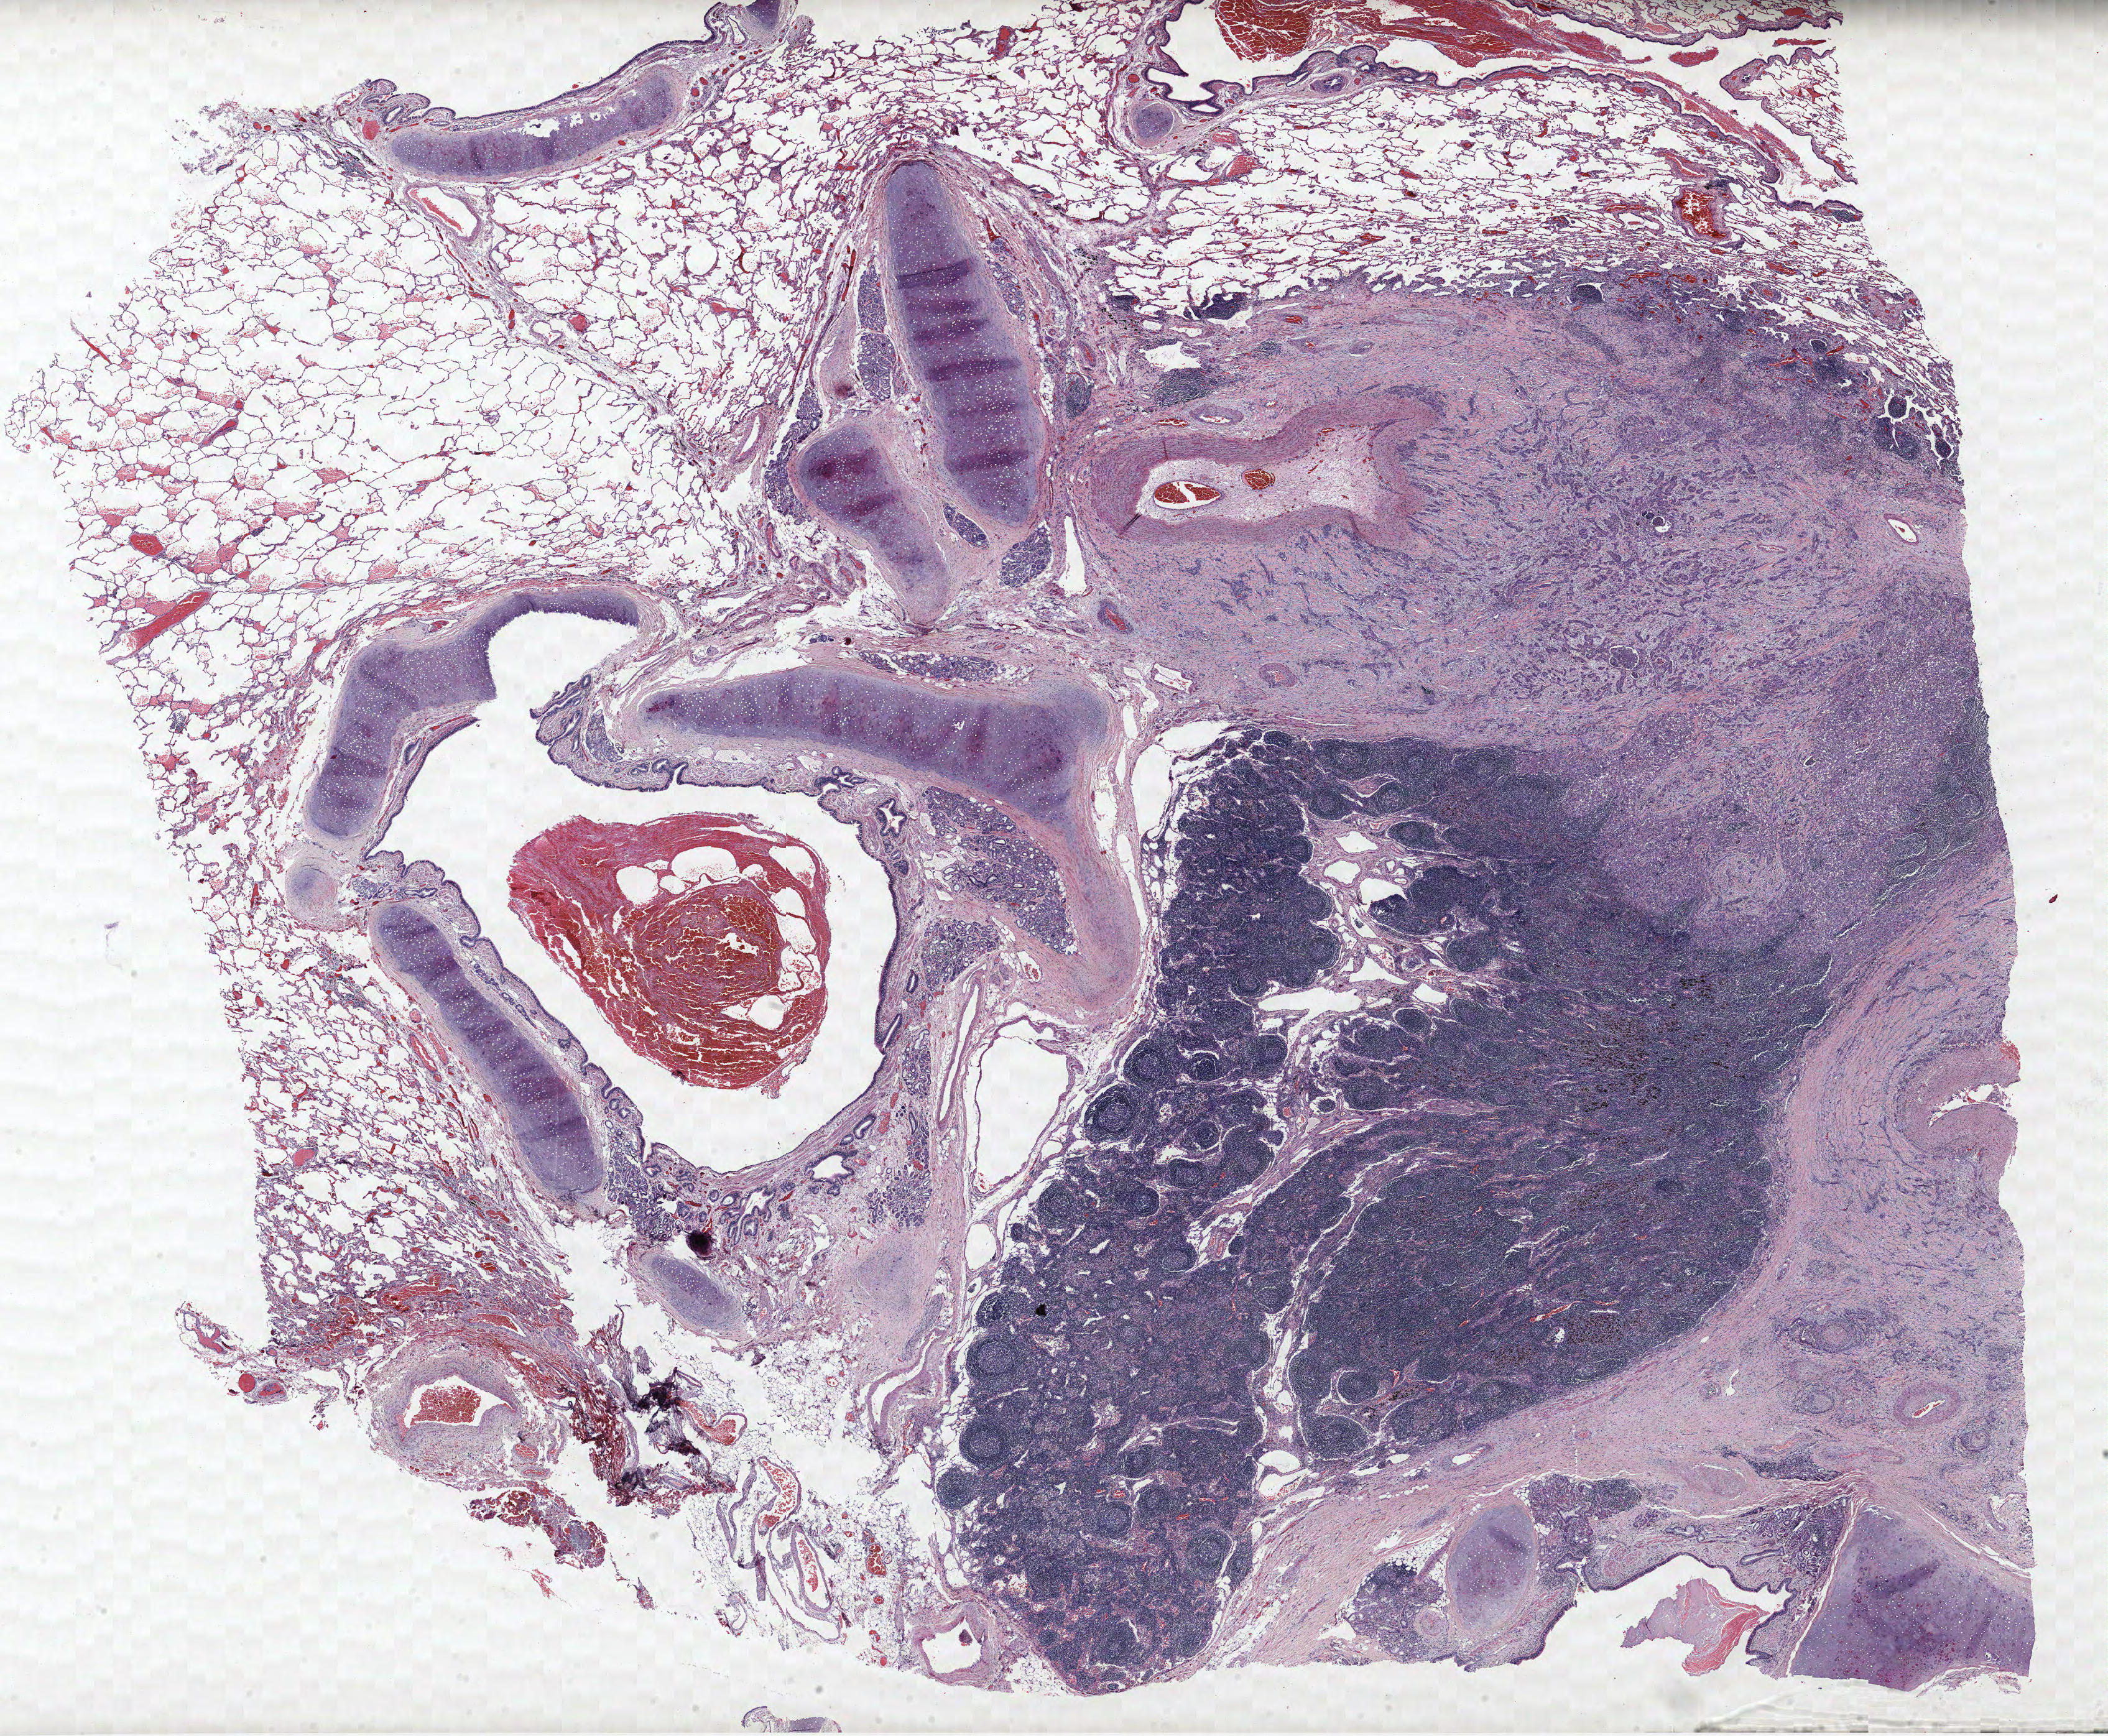
Hematoxylin and eosin (H&E) stained whole-slide image — low-resolution overview of the scanned area, about 27.1 x 22.3 mm (slide scanned at 40x), FFPE section, lung tissue. Female, age 62 at enrolment. Former smoker at enrolment. Grade: poorly differentiated (G3).
Tumour size (pathology): 50 mm. Stage (AJCC 6th edition): IIIB. Primary tumour location (clinical record): left hilum. Participant's lung-cancer diagnosis: Squamous cell carcinoma, NOS.